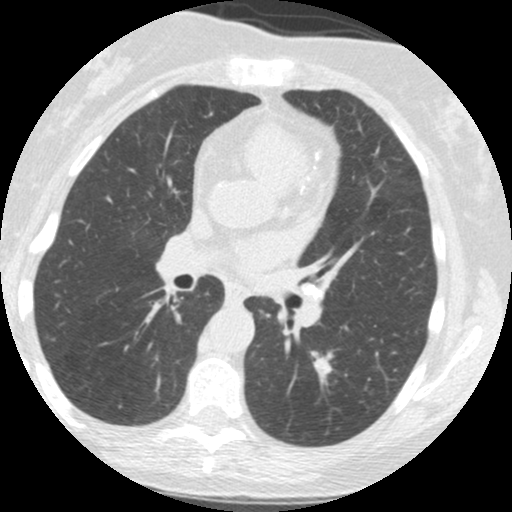
Low-dose screening chest CT, axial slice; first (baseline) screen; lung window (W 1500 / L -600 HU); 2.5 mm slice thickness; 120 kVp; 512 × 512 image matrix, field of view 289 × 289 mm. Female, age 61 years at enrolment. Current smoker at enrolment.
Expert-annotated lung lesion, bounding box (x1, y1, x2, y2) in pixels: (302, 339, 350, 392). Screening reader's record for this exam (one nodule recorded; not confirmed to be the boxed lesion): non-calcified nodule or mass ≥4 mm, left lower lobe, 12 × 11 mm, spiculated (stellate) margins, soft tissue attenuation. Later outcome: lung cancer diagnosed 440 days after this screen (after the second annual screen) — squamous cell carcinoma, NOS, left lower lobe, moderately differentiated (G2), stage IA (AJCC 6th edition), 12 mm at pathology.